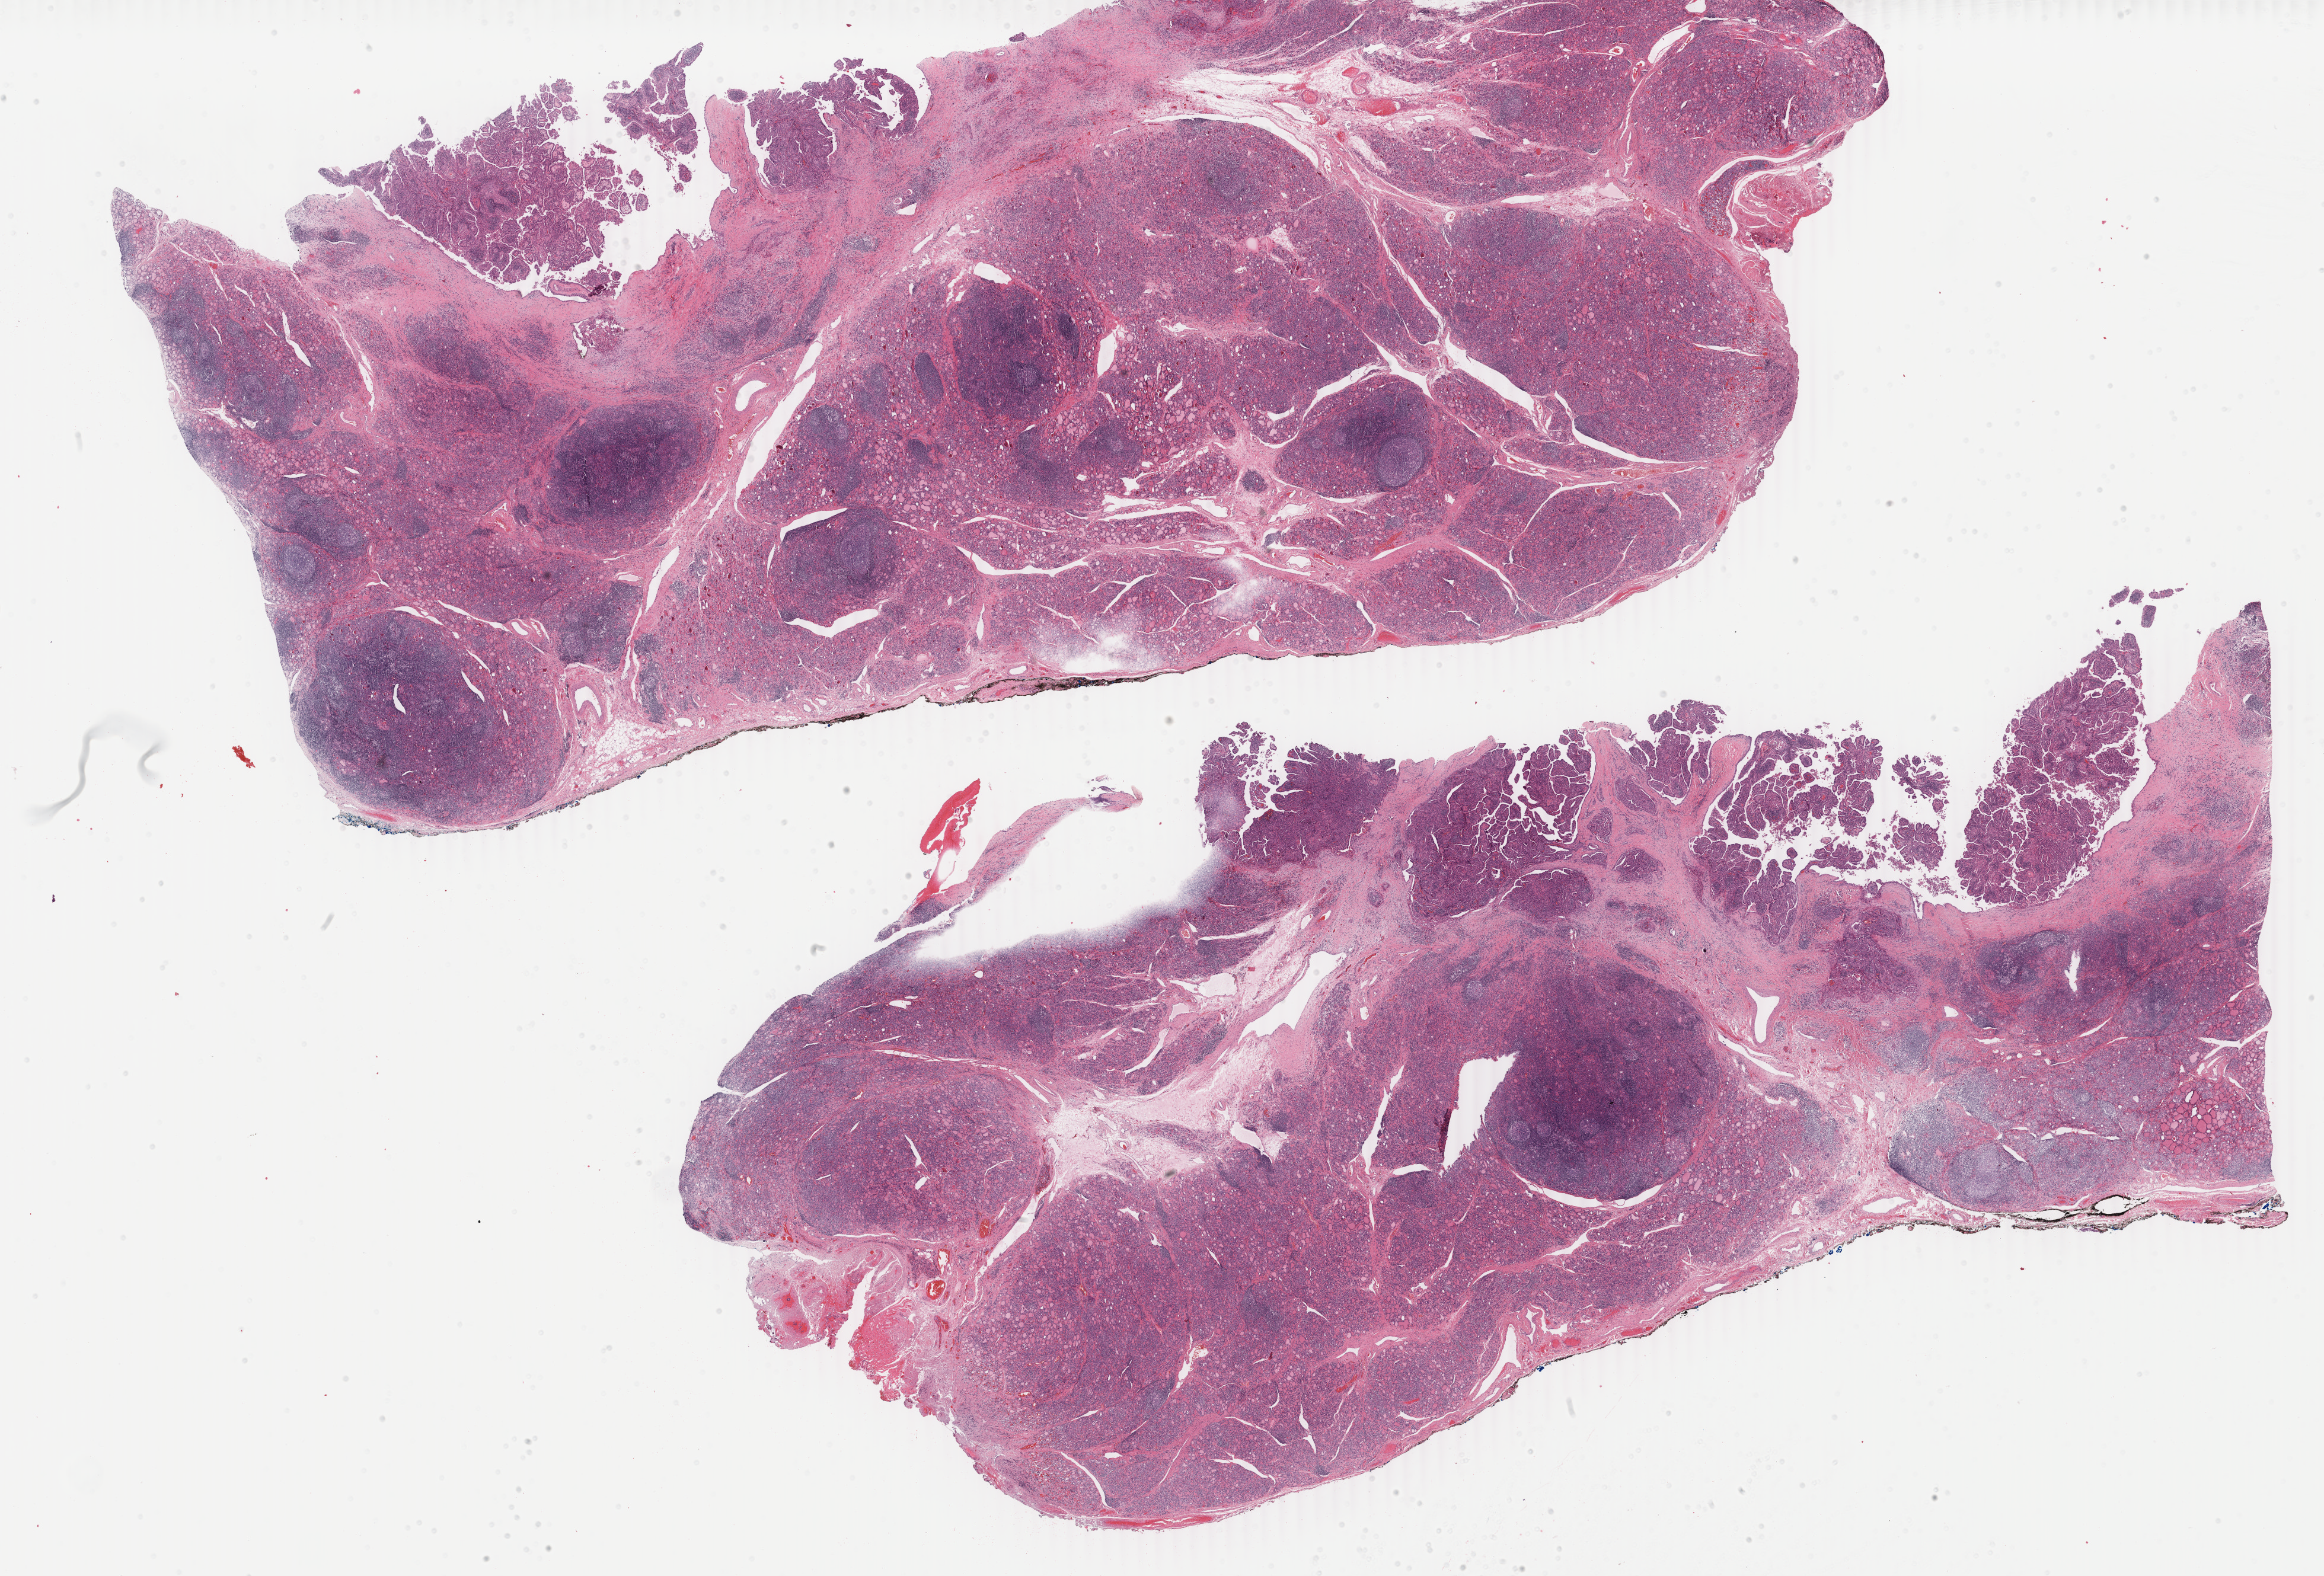
H&E-stained whole-slide image, a low-resolution overview of the entire scanned area, about 31.2 x 21.1 mm (slide scanned at 40x), formalin-fixed paraffin-embedded (FFPE) diagnostic section, sample: primary tumour, thyroid. Female, age 27 years at initial diagnosis.
- AJCC pathologic stage: I (6th edition)
- diagnosis: Papillary adenocarcinoma, NOS (thyroid gland)
- laterality: right